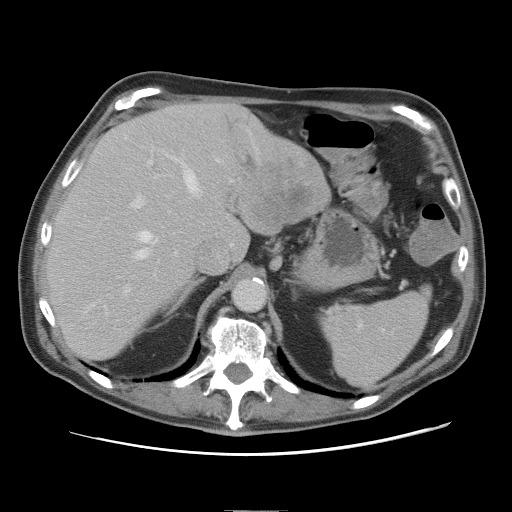
Contrast-enhanced abdominal CT, one axial slice; slice 55 of 89 in the series (ordered by position); 120 kVp; intravenous contrast given; soft-tissue window (W 400 / L 40 HU); 512 × 512 image matrix, field of view 375 × 375 mm. Male patient, age 69 years. Case-level facts recorded for this patient, not image findings: diagnosis: colorectal cancer liver metastases, imaged before liver resection; multiple liver metastases: no; largest metastasis: 8.5 cm.
Outlined on this slice (outlined manually by an expert reader):
- hepatic veins: bounding box [x1, y1, x2, y2] px = [132, 157, 203, 260]
- liver: [49, 104, 329, 360]
- planned liver remnant (the part of the liver to remain after resection): [49, 103, 247, 360]
- portal vein (with intrahepatic branches): [125, 146, 259, 292]
- liver metastasis: [250, 160, 316, 232]